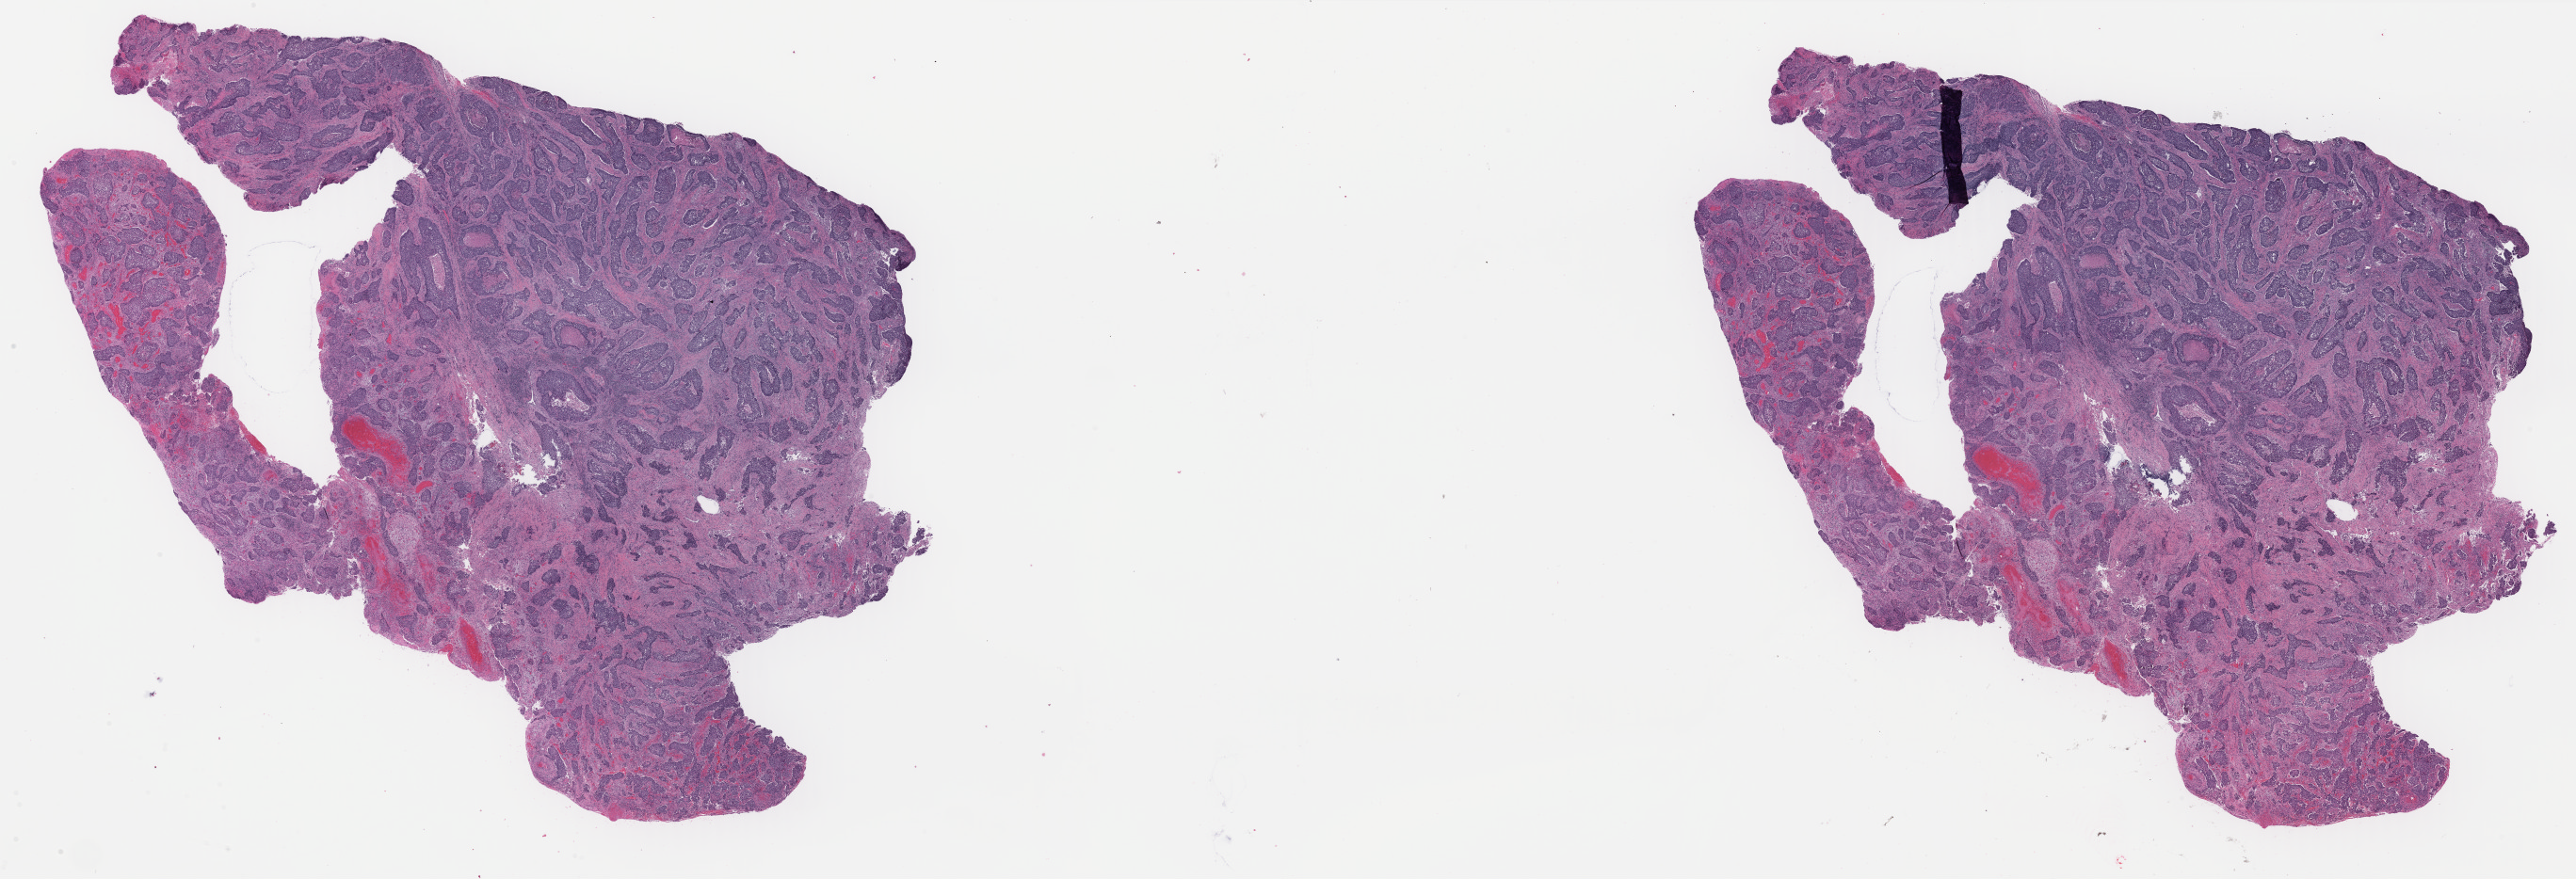
Digitized H&E tissue section (whole slide) — whole scanned area (about 43.3 x 14.8 mm, slide scanned at 40x) shown as a low-resolution overview; formalin-fixed paraffin-embedded (FFPE) diagnostic section; sample: primary tumour, head and neck. Male, age 50 years at initial diagnosis. Histologic grade: G2 (moderately differentiated).
AJCC pathologic stage: IVB (7th edition). Pathologic diagnosis: Squamous cell carcinoma, keratinizing, NOS (oropharynx, NOS).